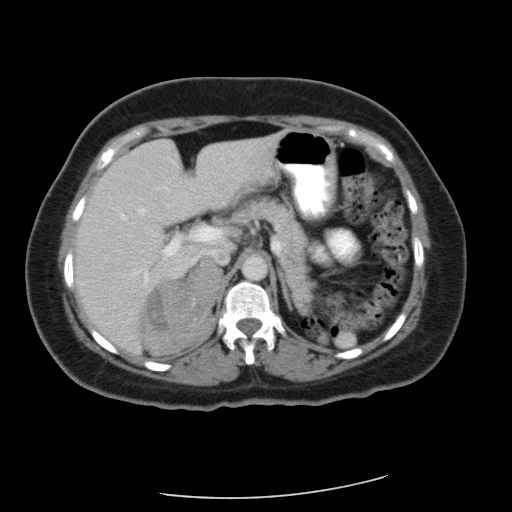
Contrast-enhanced abdominal CT, one axial slice; slice 39 of 56 in the series (ordered by position); 120 kVp; soft-tissue window (W 400 / L 40 HU); 5 mm slice thickness; 512 × 512 image matrix, field of view 400 × 400 mm. Patient: female, 58 years. From the clinical record (not read from this slice): diagnosis: adrenocortical carcinoma; tumour side: right adrenal; tumour size at pathology: 9 cm; Ki-67 index: 25 %; stage (as recorded): 3.
Outlined on this slice (semi-automatic segmentation, software-assisted and operator-edited):
- mass: bounding box [x1, y1, x2, y2] px = [145, 264, 219, 354]